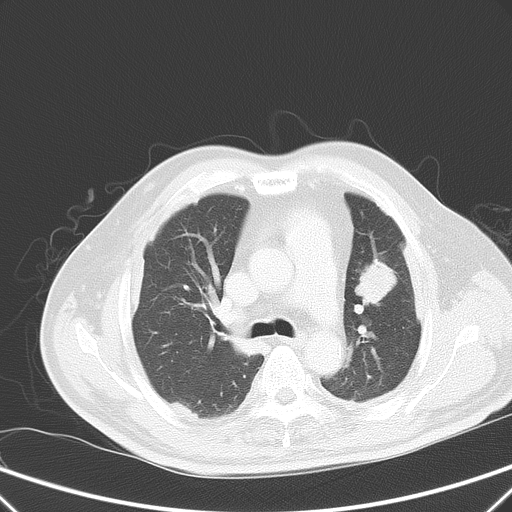
Chest CT, one axial slice; position 39 of 59 along the scan axis; 120 kVp; intravenous contrast given; lung window (W 1500 / L -600 HU); 5 mm slice thickness; 512 × 512 image matrix, field of view 357 × 357 mm. Male patient, age 66 years. From the clinical record (not read from this slice): clinical TNM (as recorded): T1c N3 M1a.
Structures marked on this image (rectangle marked by the reading radiologist):
- lung tumour (recorded histology: squamous cell carcinoma): box from (x=351, y=259) to (x=401, y=309) px